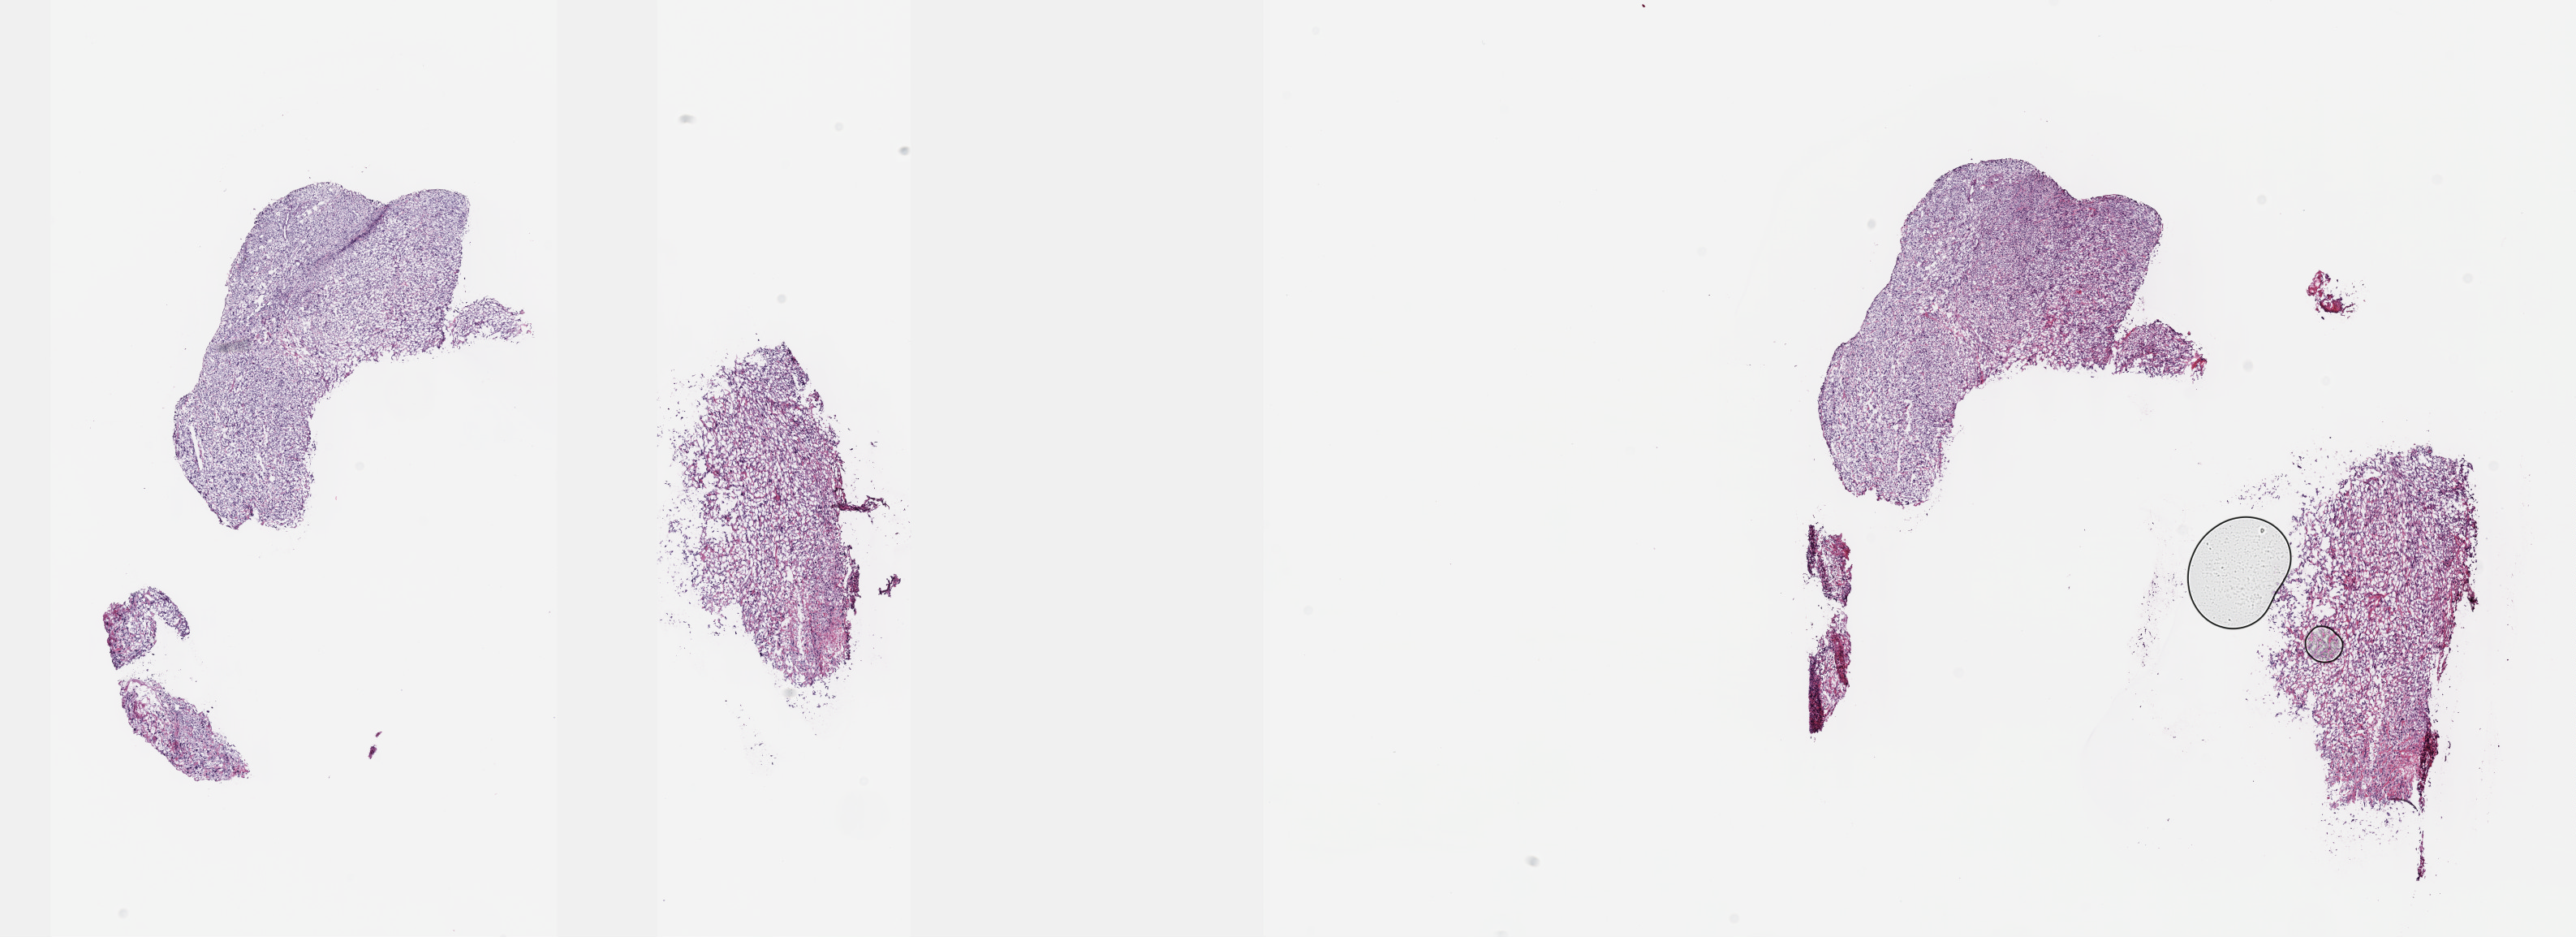
Whole-slide histology image, H&E-stained, low-resolution overview of the scanned area, about 25.7 x 9.3 mm; frozen section from the top of the tissue portion; sample: primary tumour, connective, subcutaneous and other soft tissues. Male, age 74 years at initial diagnosis.
Pathologic diagnosis: Leiomyosarcoma, NOS (connective, subcutaneous and other soft tissues of lower limb and hip).